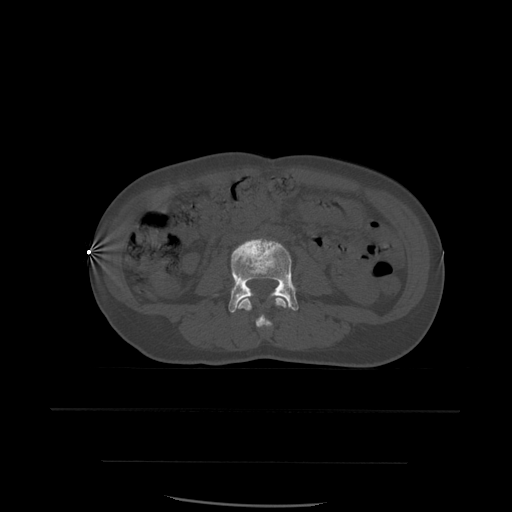
CT including the spine, one axial slice. Slice 180 of 574 in the series (ordered by position). Bone window (W 1800 / L 400 HU). 1.25 mm slice thickness. 512 × 512 image matrix, field of view 392 × 392 mm. Patient age 48 years. Case-level facts recorded for this patient, not image findings: primary cancer: lung.
Outlined on this slice (semi-automatically segmented with operator editing):
- L3 vertebra: bounding box <235,297,287,329> (left, top, right, bottom; pixels)
- L4 vertebra: <229,238,299,313>